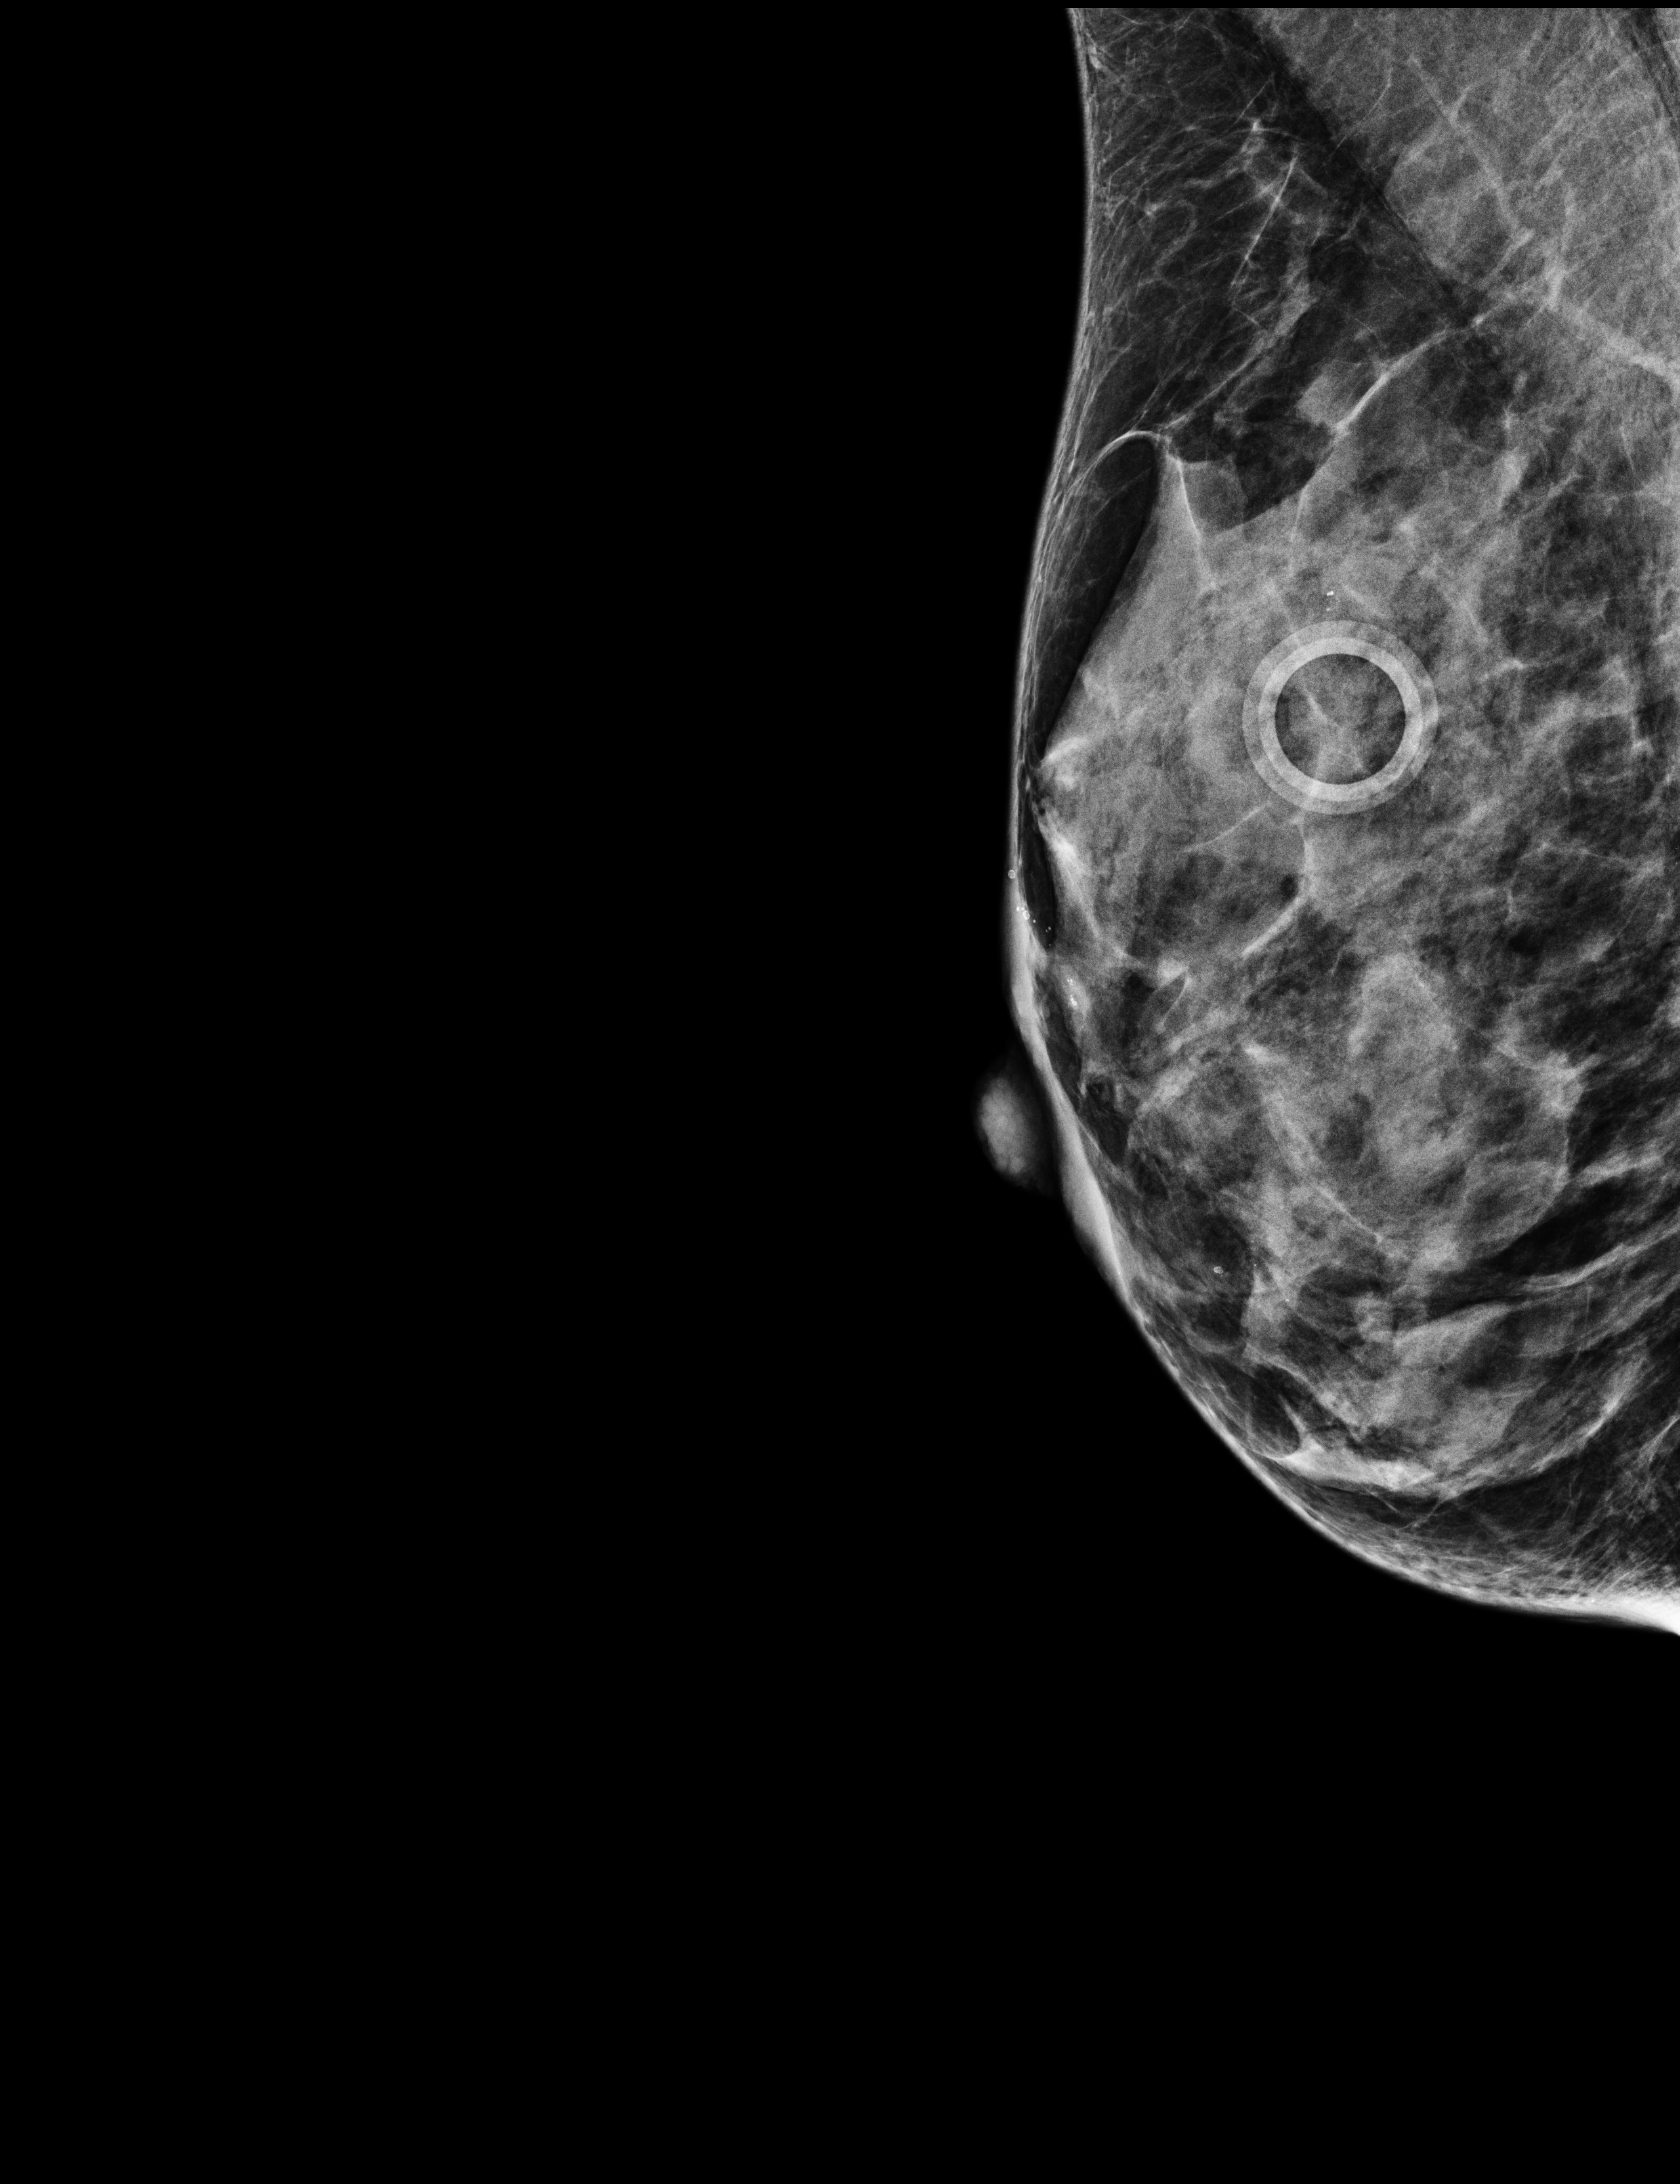
Full-field digital mammogram (FFDM); right breast; medio-lateral oblique projection; annual screening mammography examination. Female patient, age 56 years.
Breast density at the screening exam (both breasts): heterogeneously dense (BI-RADS density category c). Final BI-RADS category for the screening round (tomosynthesis exam, both breasts): category 2. Recall: recalled for additional imaging after this screen.